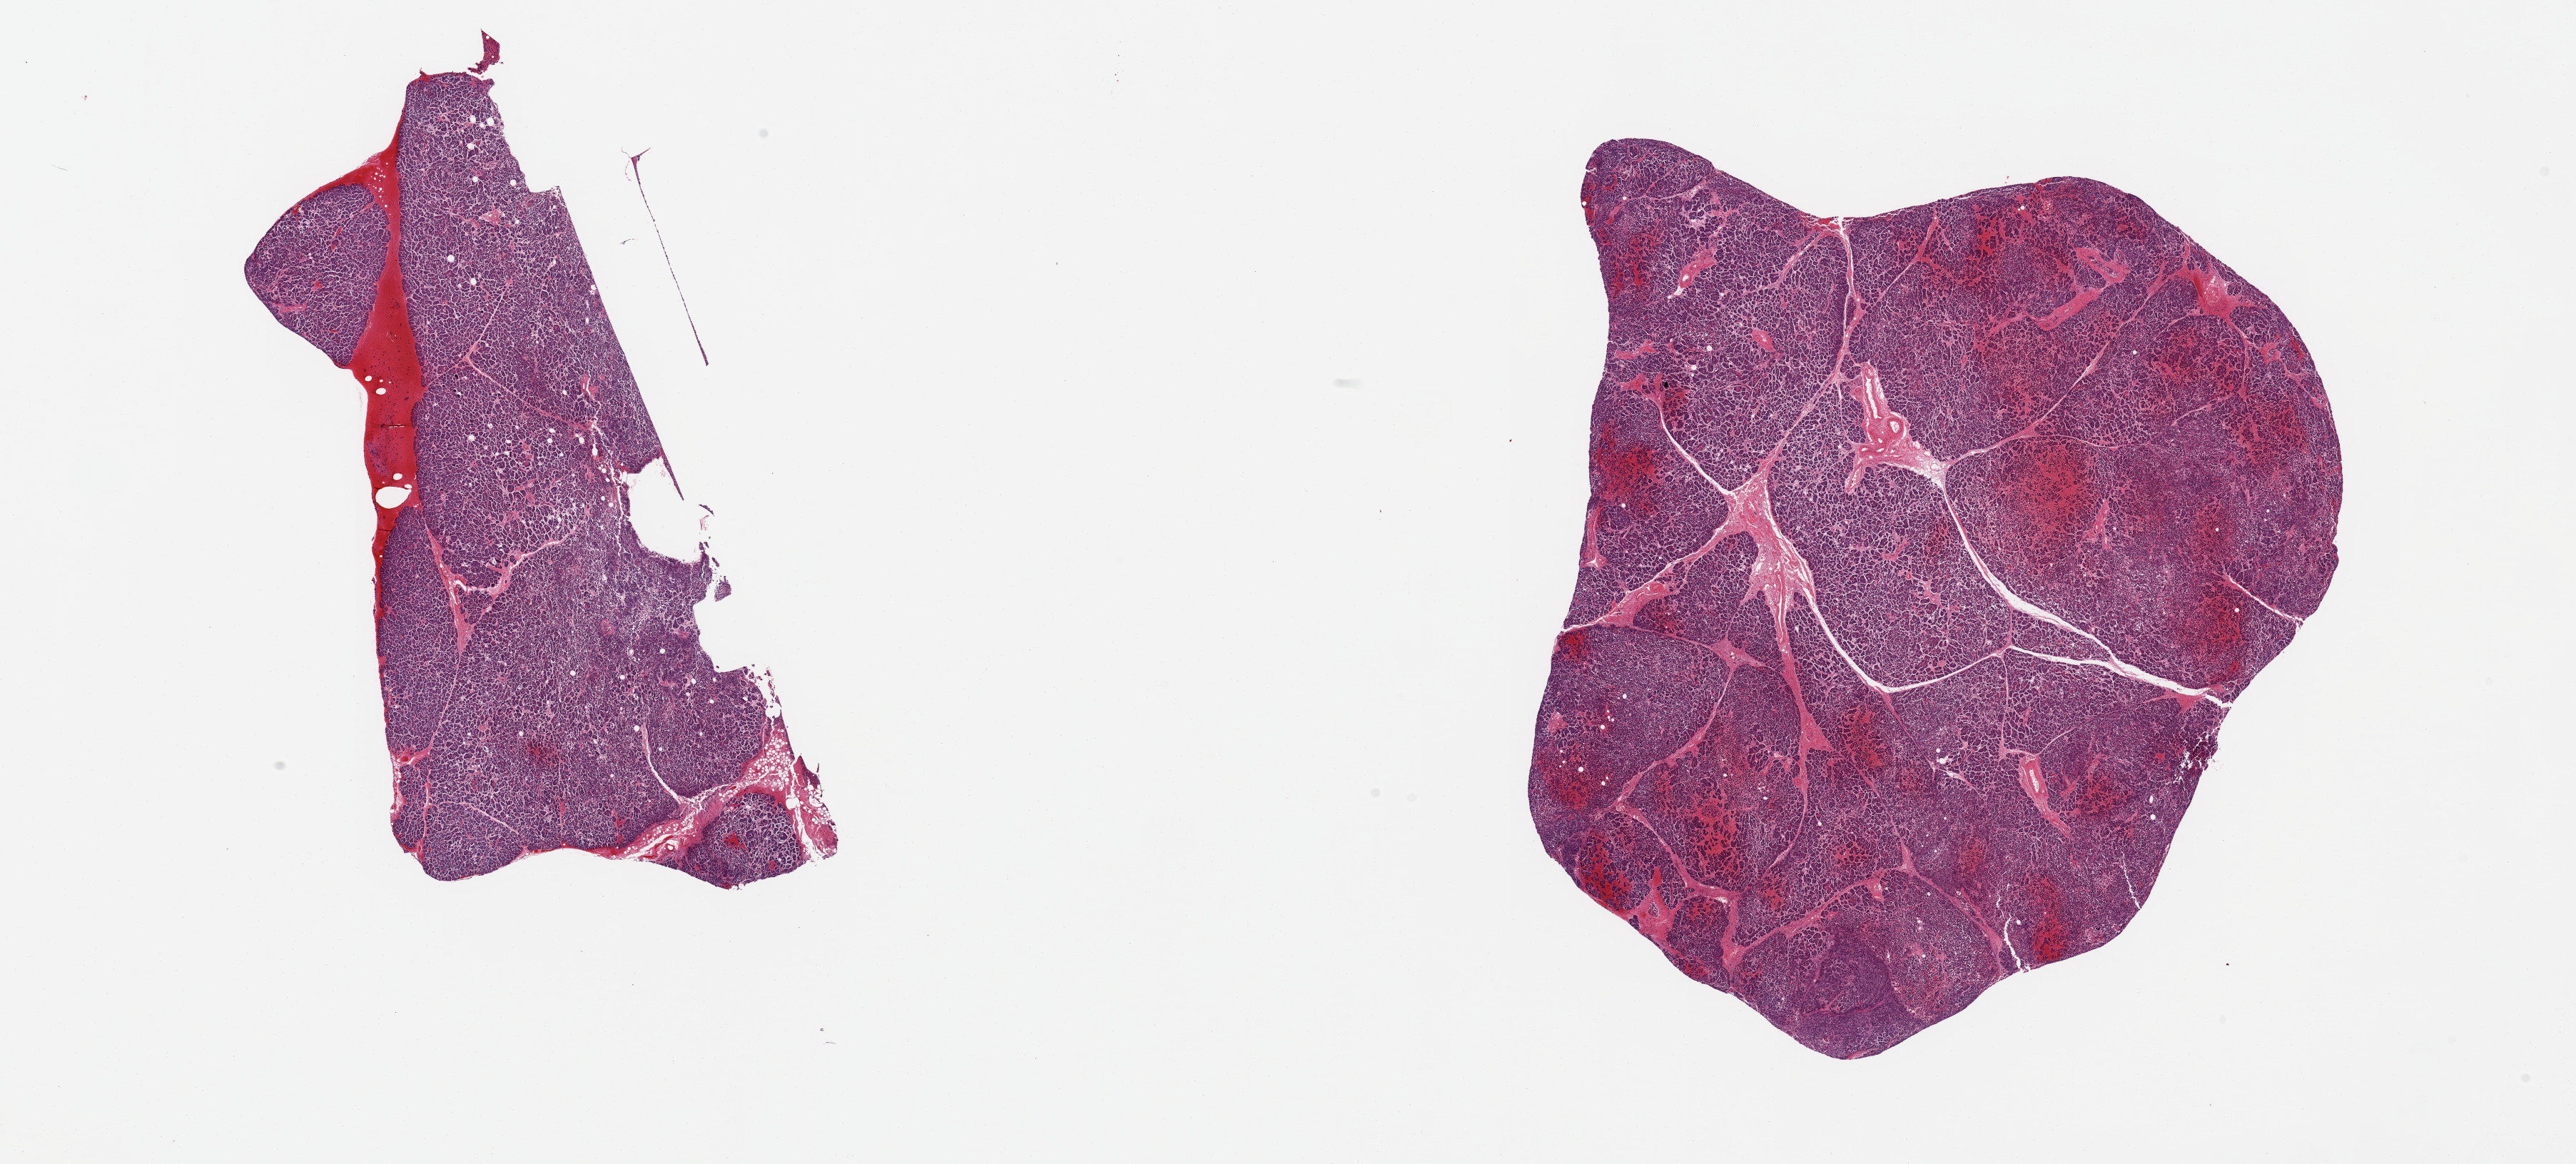
Whole-slide image, haematoxylin and eosin stain, brightfield — shown as a low-resolution overview of the whole scanned area (about 28.5 x 12.9 mm), PAXgene-fixed paraffin-embedded (PFPE) section, sampled site (target tissue): pancreas, donor tissue sample.
Pathologist's review note for this sample: 2 pieces; moderate to severe autolysis, congestion/hemorrhage.